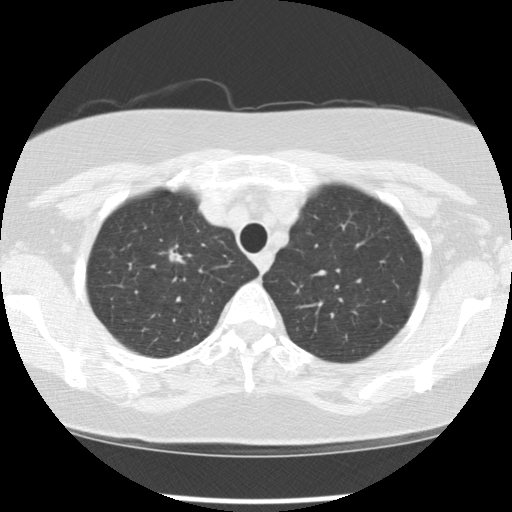
Axial slice from a low-dose chest CT screening exam, first (baseline) screen, lung window (W 1500 / L -600 HU), 120 kVp, 512 × 512 image matrix, field of view 318 × 318 mm. Female, age 65 years at enrolment. Current smoker at enrolment.
Lesion marked by an expert reader, bounding box (x1, y1, x2, y2) in pixels: (146, 230, 198, 281). The screening reader recorded 2 non-calcified nodules or masses ≥4 mm on this exam (right upper lobe, right upper lobe); which of them this box marks is not recorded. Lung cancer was diagnosed 183 days after this screen: large cell carcinoma, NOS, right upper lobe, poorly differentiated (G3), stage IA (AJCC 6th edition), 20 mm at pathology.